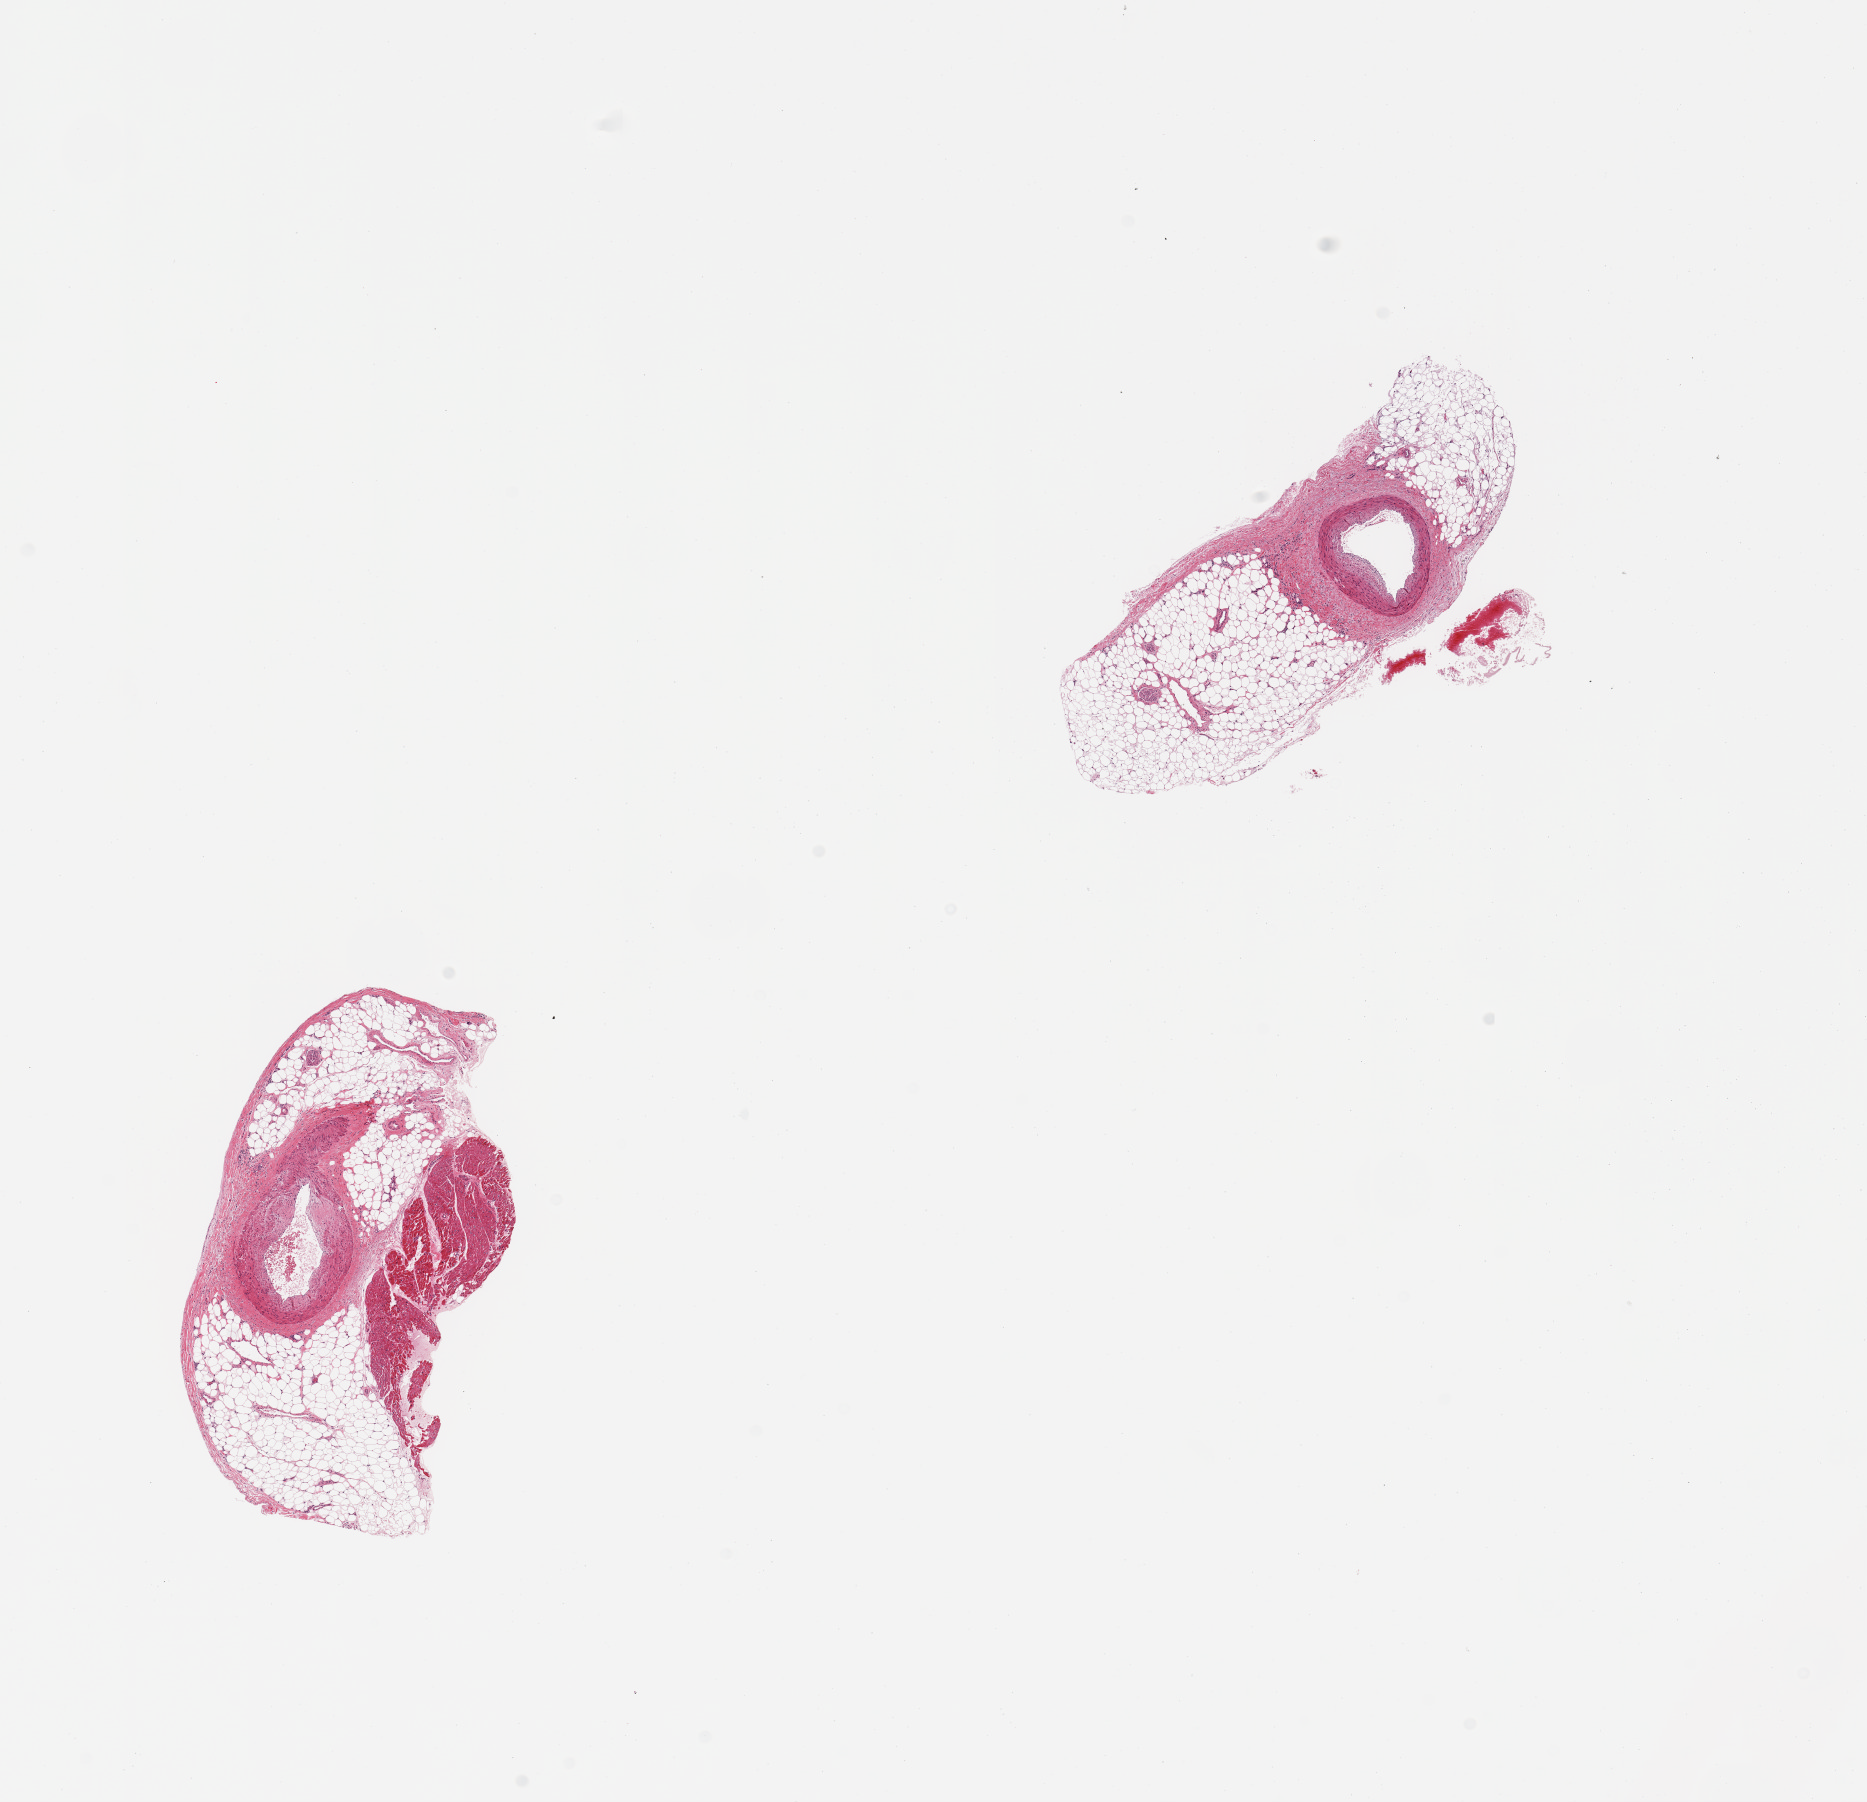
Digitized haematoxylin and eosin-stained section, brightfield, shown as a low-resolution overview of the whole scanned area (about 14.8 x 14.3 mm); PAXgene-fixed, paraffin-embedded tissue; target tissue: coronary artery; tissue donor sample. Donor: male.
Reviewer comment on this tissue sample: 2 pieces; mildly sclerotic artery, diameter 1.5mm. Most of specimen is external fat and 1 large (1.7 sq mm) piece of myocardium. Artery comprises <40% of sampled area.